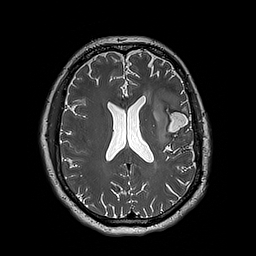
Brain MRI from a brain-tumour surgery series, one axial slice. Slice 87 of 192 in the series (ordered by position). 1 mm slice thickness. 256 × 256 image matrix, field of view 250 × 250 mm. From the clinical record (not read from this slice): histopathology: Astrocytoma; WHO grade: 3; IDH mutation: yes.
Structures marked on this image (manually delineated by an expert):
- tumour: bounding box (x1, y1, x2, y2) in pixels: (153, 92, 180, 145)